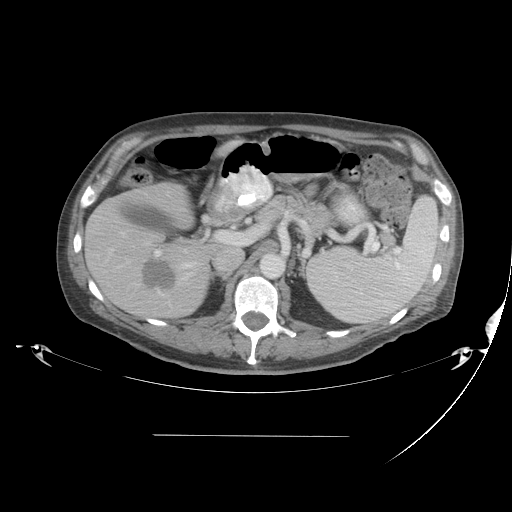
Contrast-enhanced abdominal CT, one axial slice; position 25 of 48 along the scan axis; intravenous contrast given; soft-tissue window (W 400 / L 40 HU); 512 × 512 image matrix, field of view 486 × 486 mm. Male patient, age 65 years. From the clinical record (not read from this slice): diagnosis: colorectal cancer liver metastases, imaged before liver resection; multiple liver metastases: yes; largest metastasis: 11 cm; disease in both lobes: yes.
Structures marked on this image (outlined manually by an expert reader):
- hepatic veins: bounding box (x1, y1, x2, y2) in pixels: (105, 231, 197, 280)
- liver: (86, 182, 216, 320)
- planned liver remnant (the part of the liver to remain after resection): (139, 182, 192, 218)
- portal vein (with intrahepatic branches): (98, 230, 234, 257)
- liver metastasis: (142, 260, 177, 289)